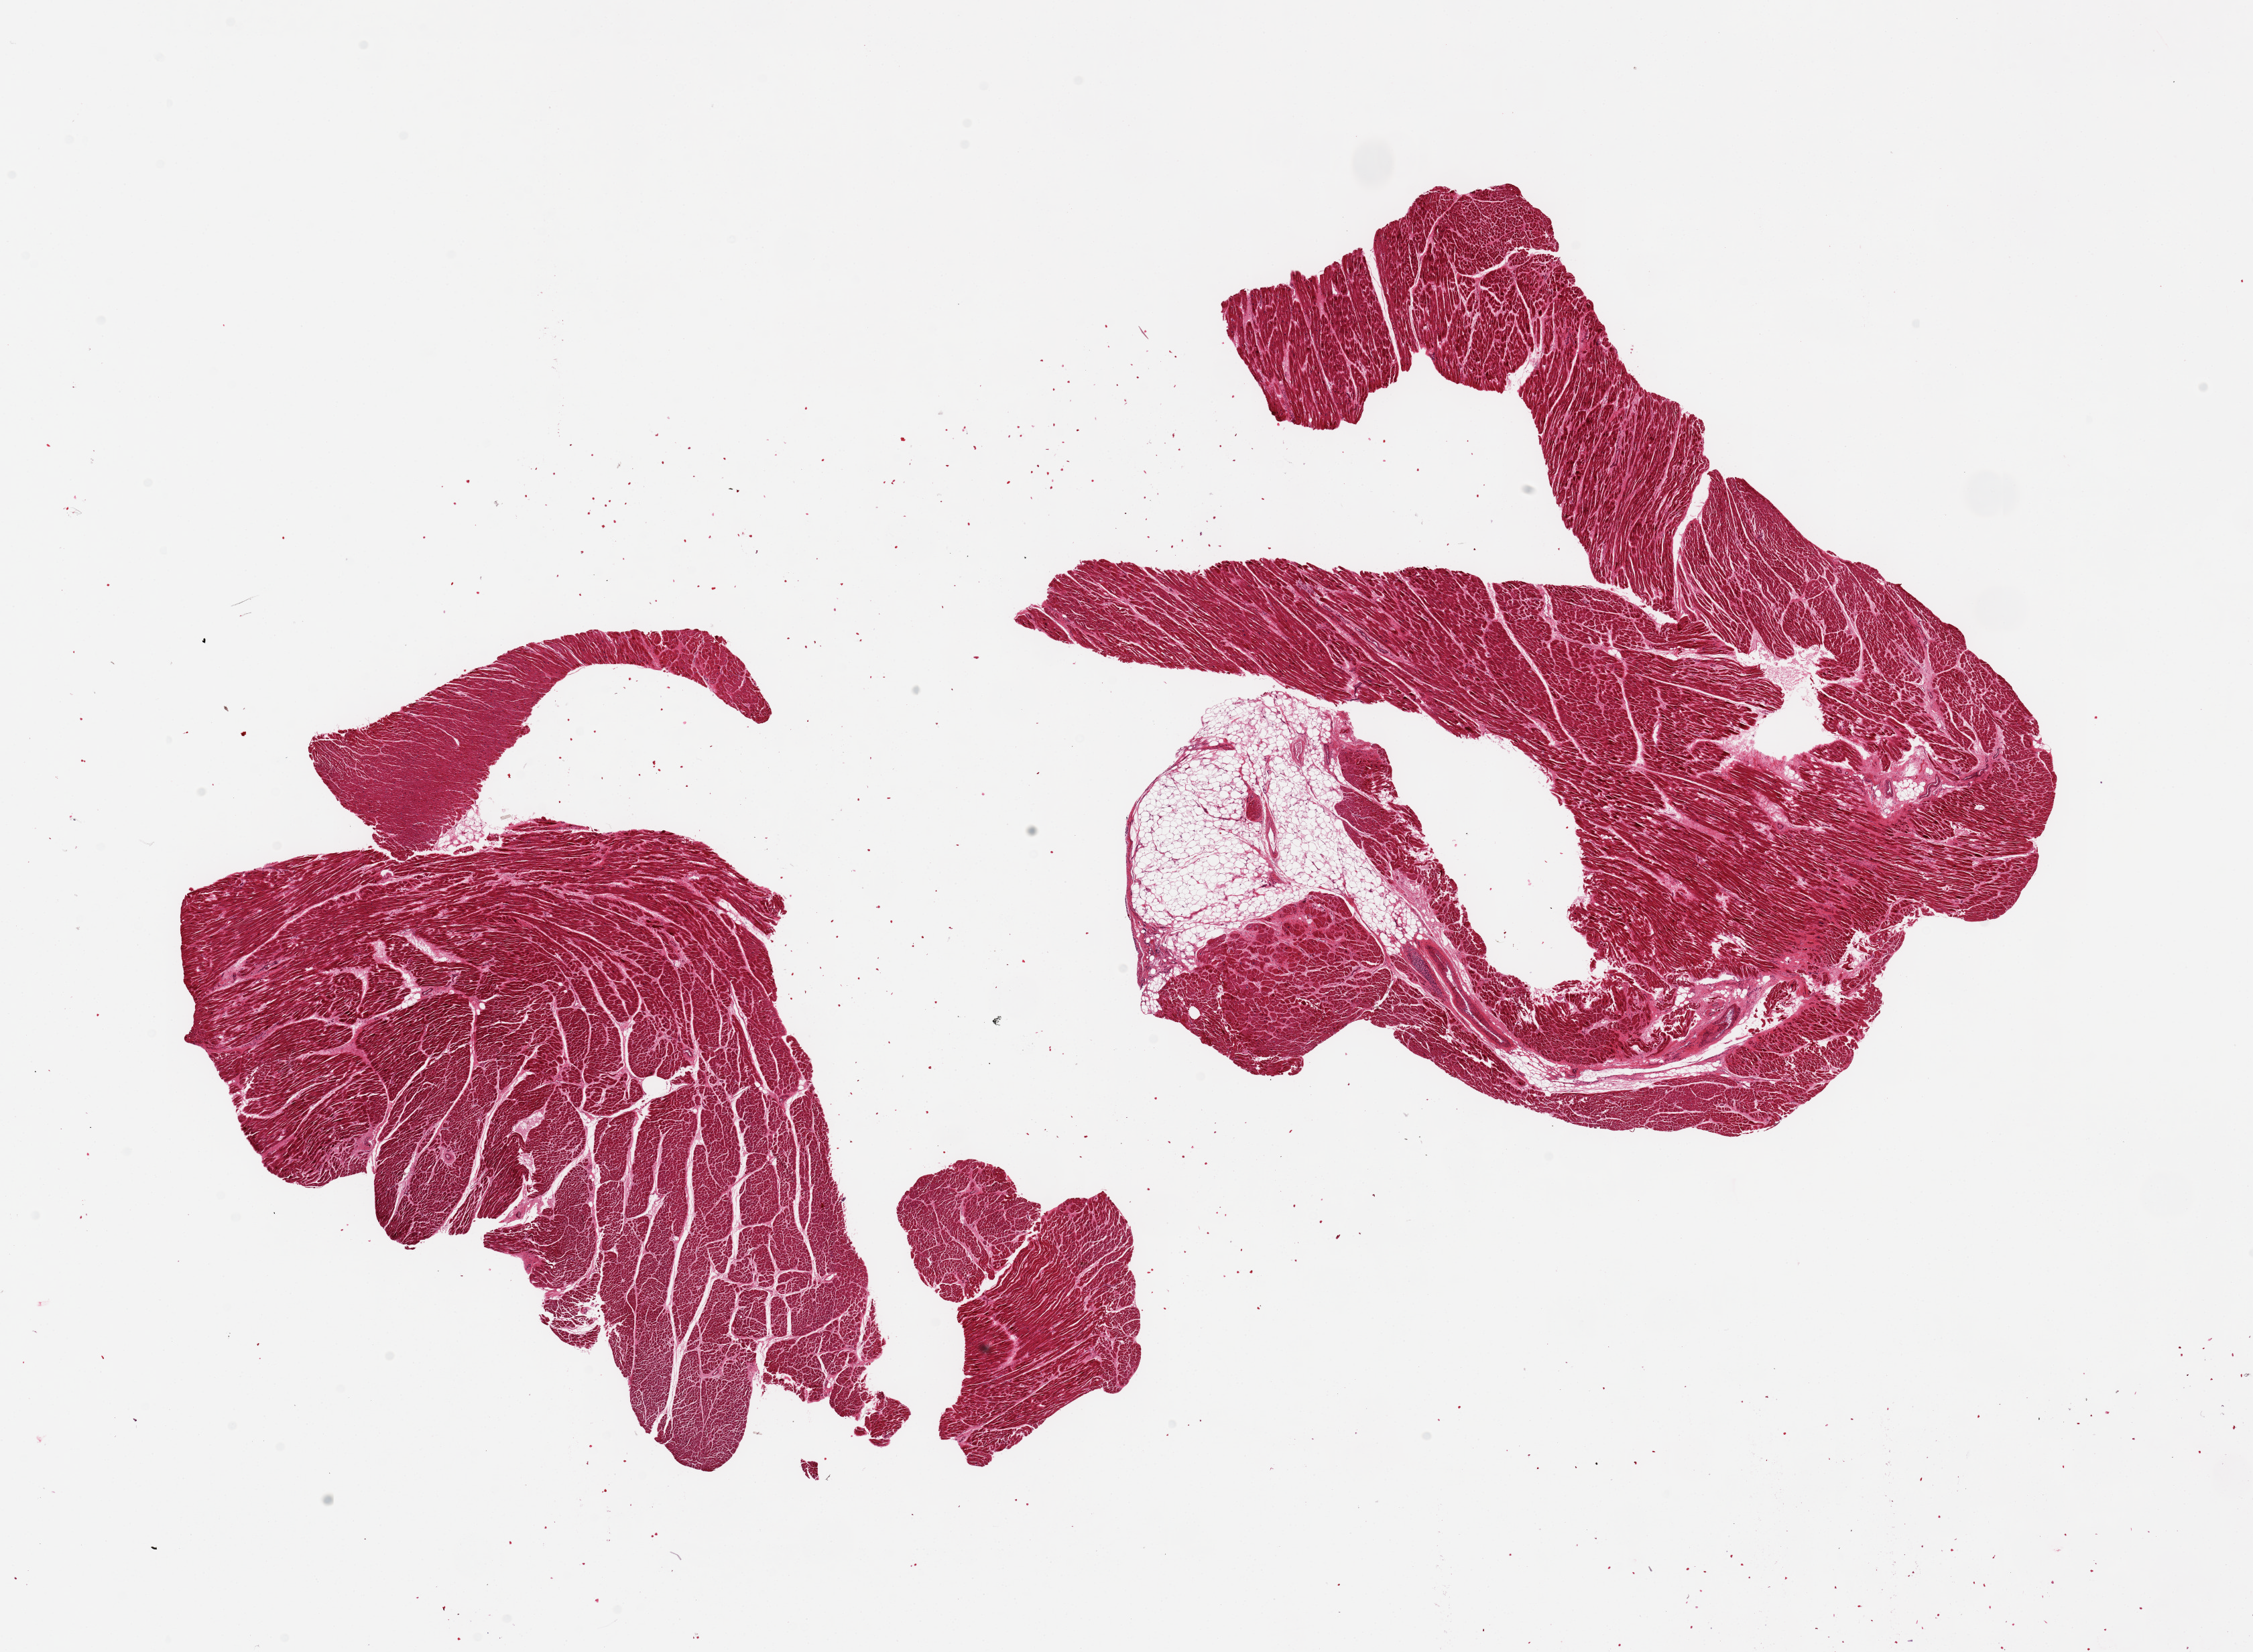
Whole-slide image, hematoxylin and eosin (H&E) stain, brightfield — shown as a low-resolution overview of the whole scanned area (about 26.6 x 19.5 mm); PAXgene-fixed paraffin-embedded (PFPE) section; section of heart (target tissue); tissue donor sample. Donor: male.
Pathologist's review note for this sample: 2 pieces, mild/moderate ischemic changes.